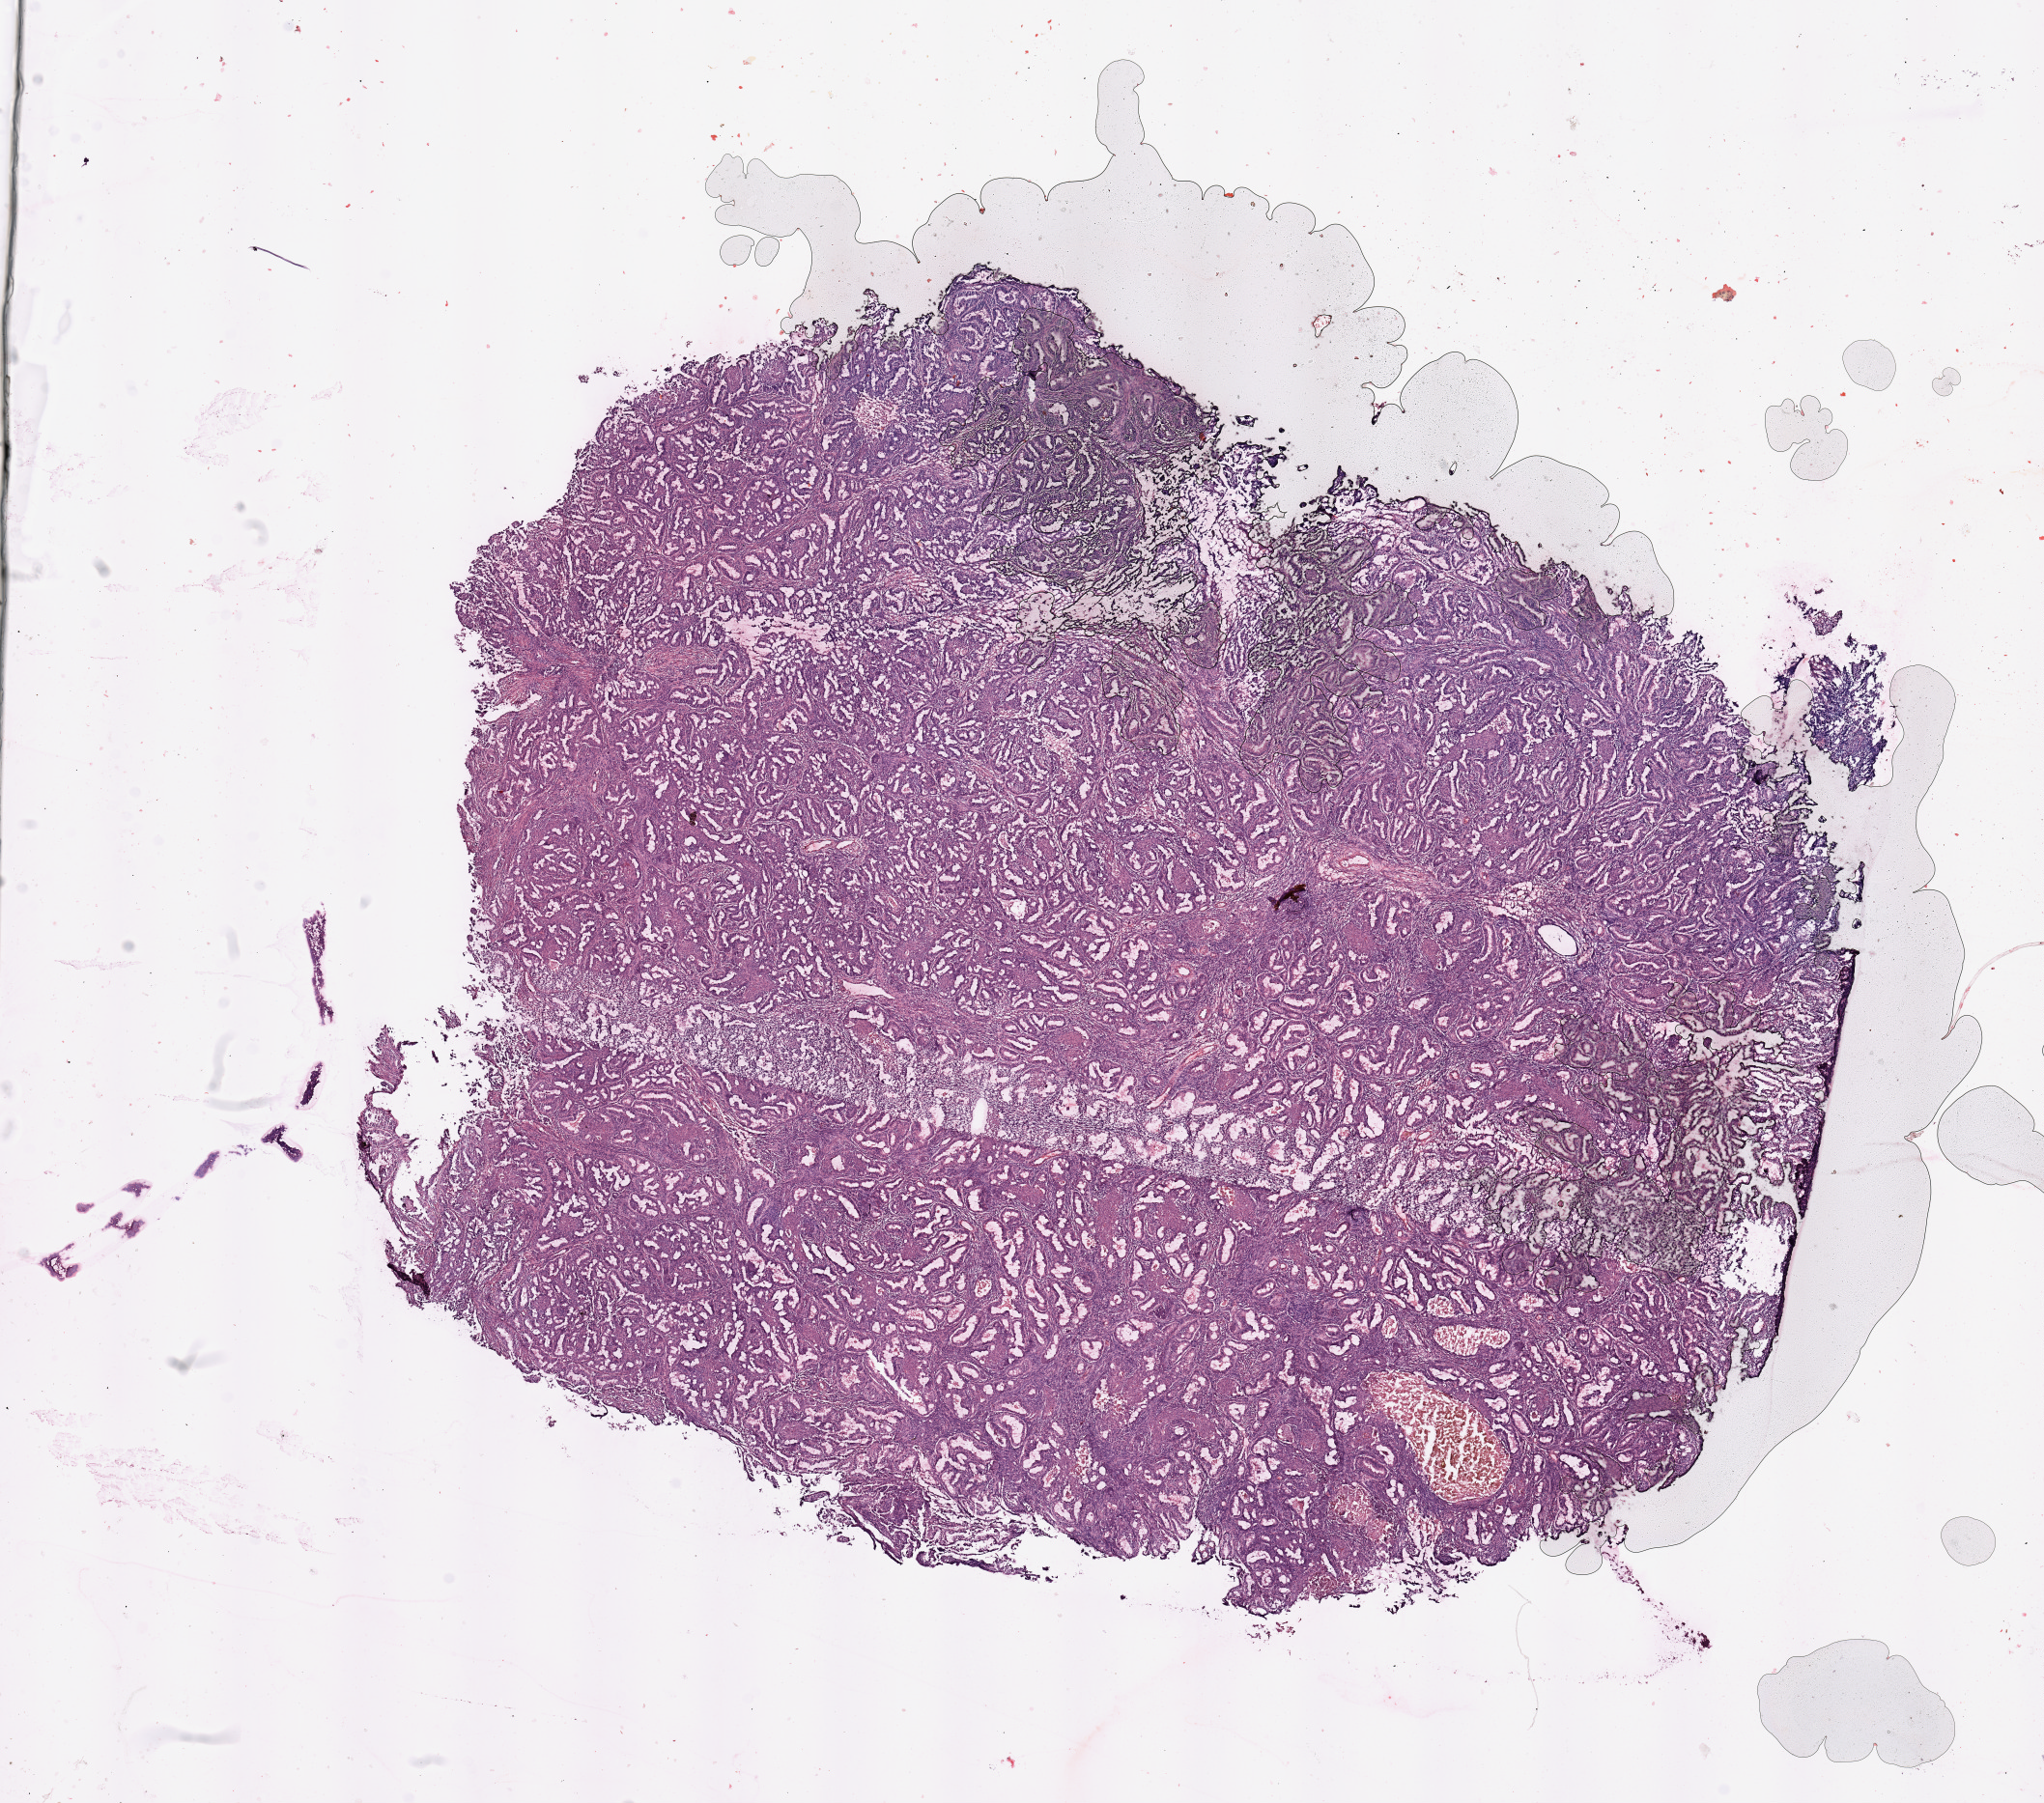
Digitized Hematoxylin and eosin (H&E) stained tissue section (whole slide), shown as a low-resolution overview of the whole scanned area (about 16.7 x 14.8 mm, slide scanned at 20x). Uterus, tumour tissue. 44-year-old female patient.
Diagnosis: Endometrioid adenocarcinoma, NOS.